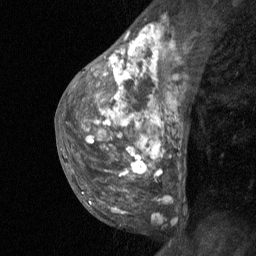
Breast MRI (dynamic contrast-enhanced), one sagittal slice; slice 36 of 64 in the series (ordered by position); dynamic contrast-enhanced study with each time point stored as its own series, time point 2 of 3 at this slice position (early post-contrast, ordered by acquisition time); 1.5 T; TE 4.8 ms, TR 27 ms; 2 mm slice thickness; 256 × 256 image matrix, field of view 180 × 180 mm. Patient: female, 36 years. From the clinical record (not read from this slice): setting: breast cancer imaged before/during neoadjuvant chemotherapy; receptor status: HR-positive, HER2-negative.
Structures marked on this image (semi-automatic segmentation, software-assisted and operator-edited):
- analysis volume of interest (the breast-tissue region the enhancement analysis was run in; not a lesion): box from (x=67, y=12) to (x=172, y=225) px
- tumour enhancement mask (voxels above the 90 % enhancement threshold inside the analysis volume of interest): (x=86, y=27)–(x=154, y=175)